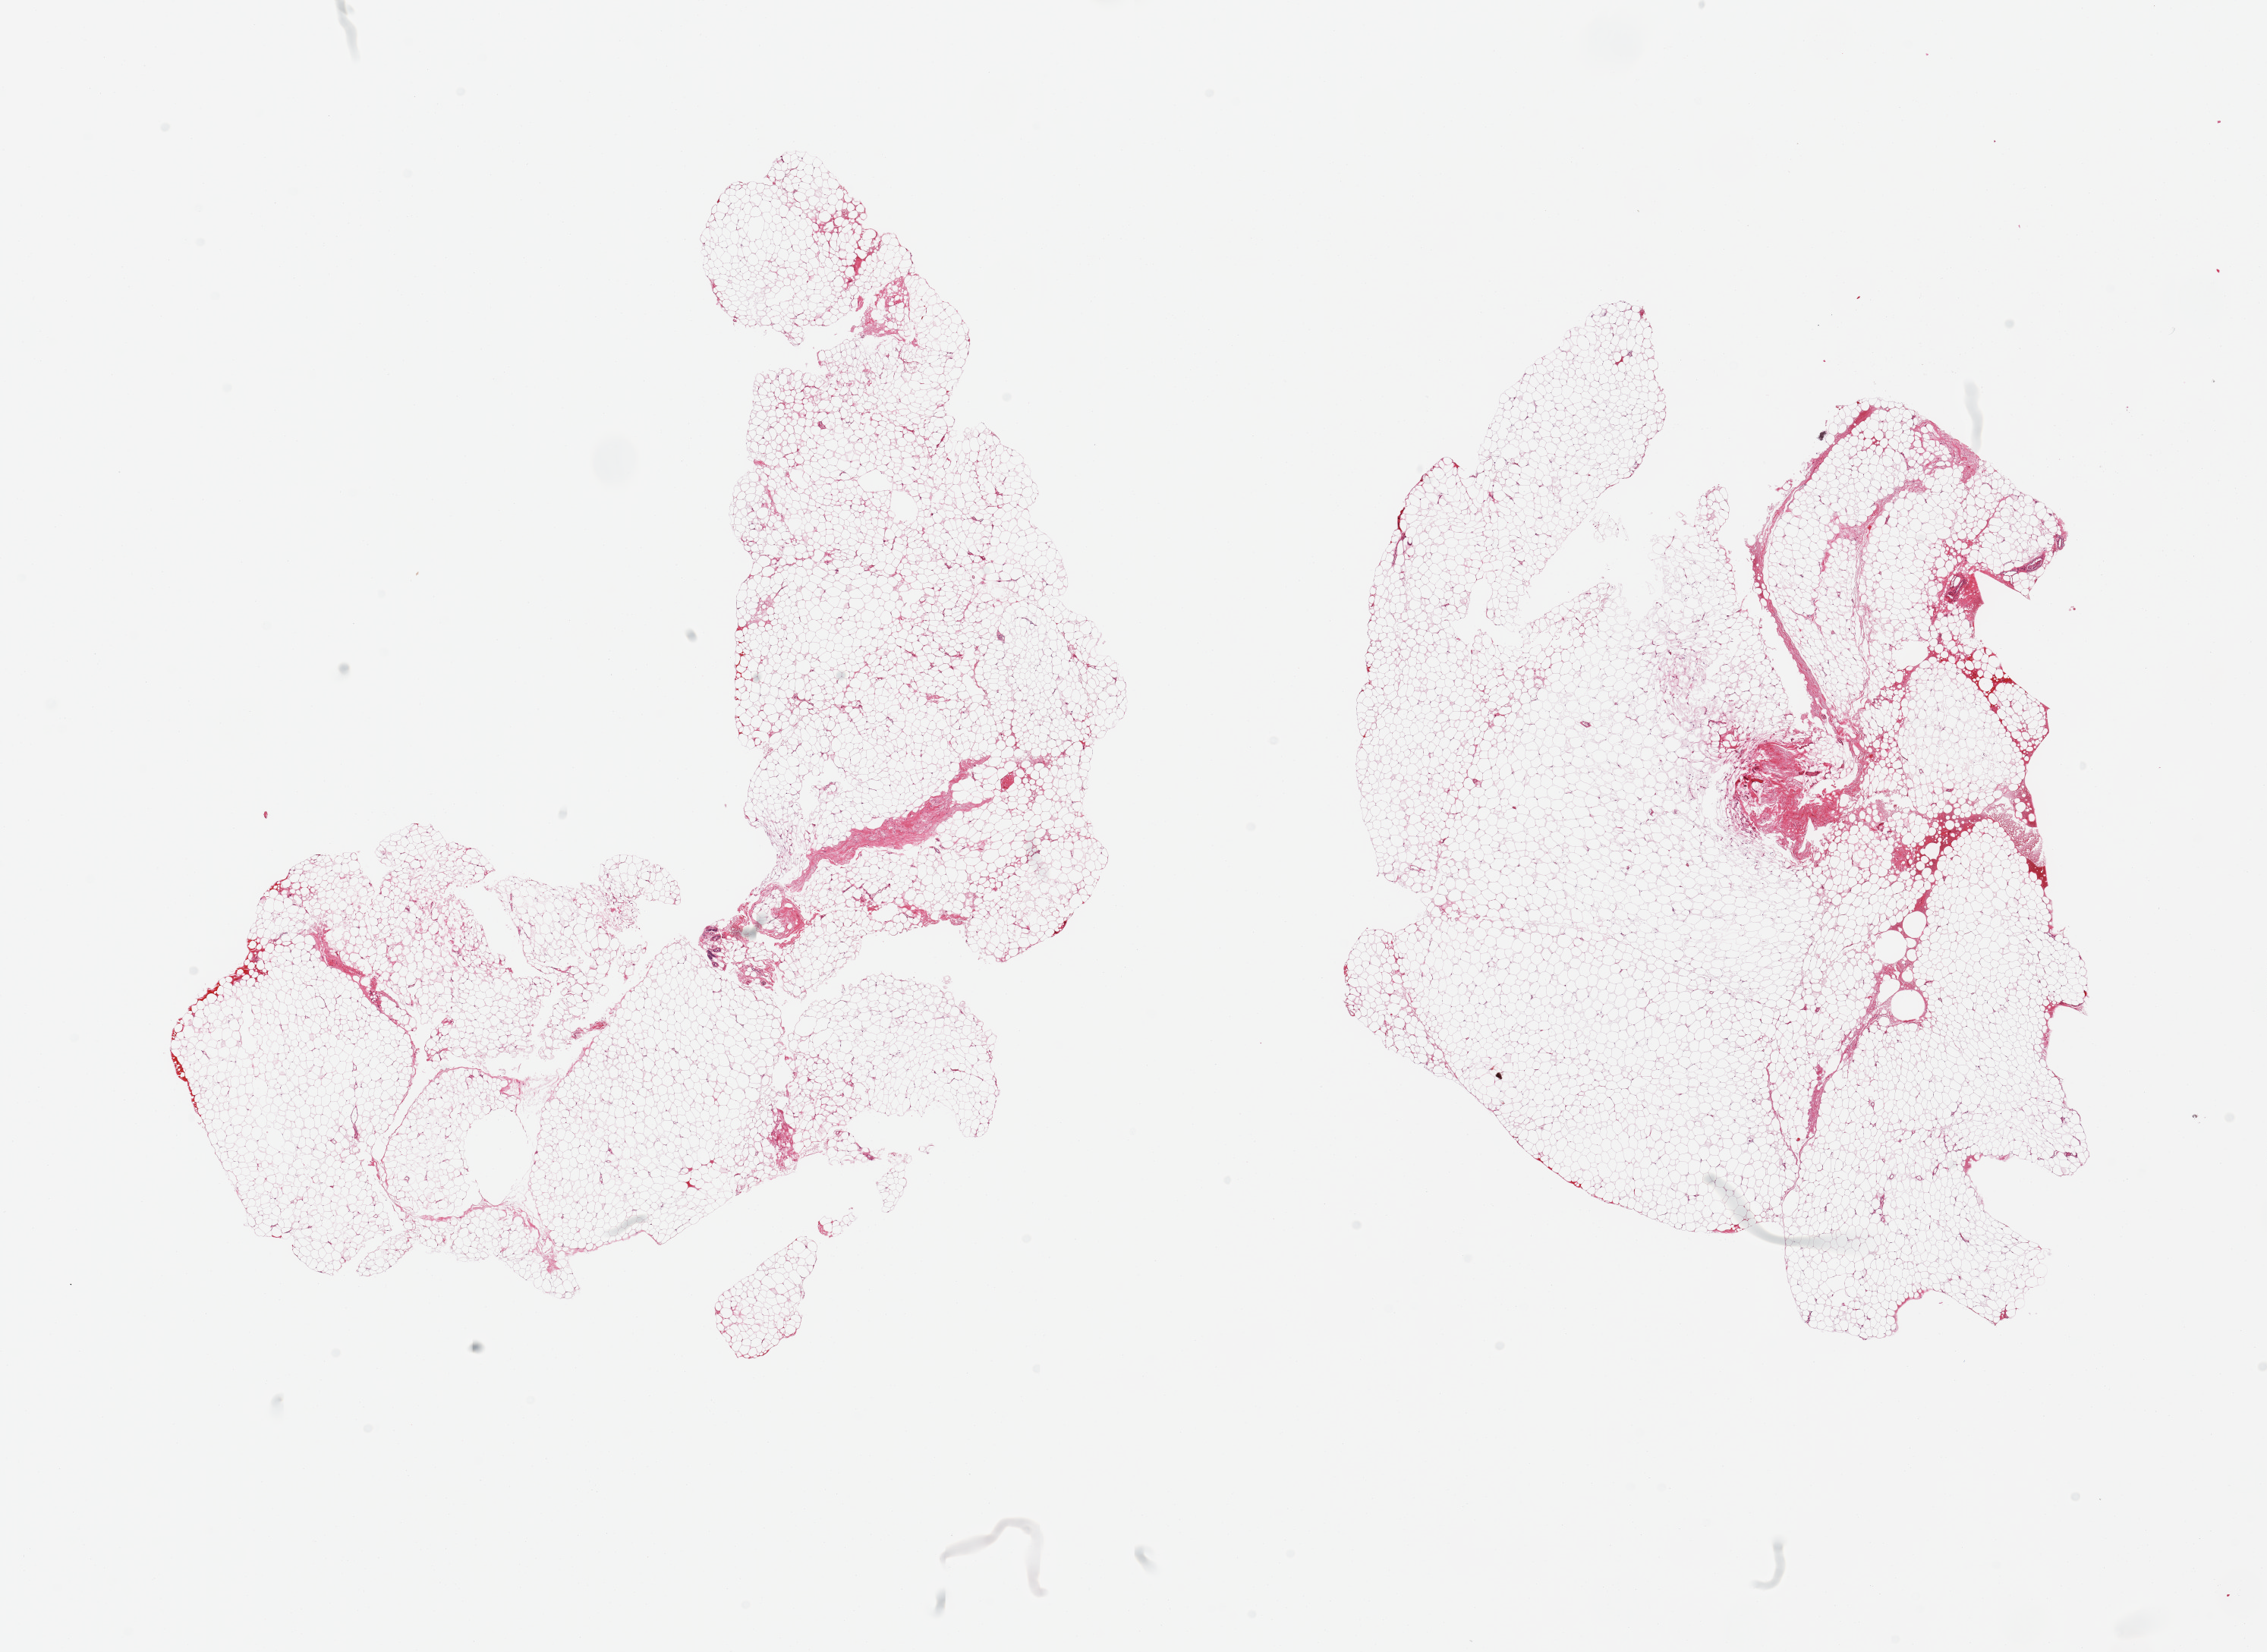
Whole-slide image, H&E stain, brightfield, shown as a low-resolution overview of the whole scanned area (about 23.6 x 17.2 mm). PAXgene-fixed, paraffin-embedded tissue. Target tissue: adipose tissue. Donor tissue sample. Donor: male.
Review note (as recorded): 2 pieces, ~5-10% fascia.